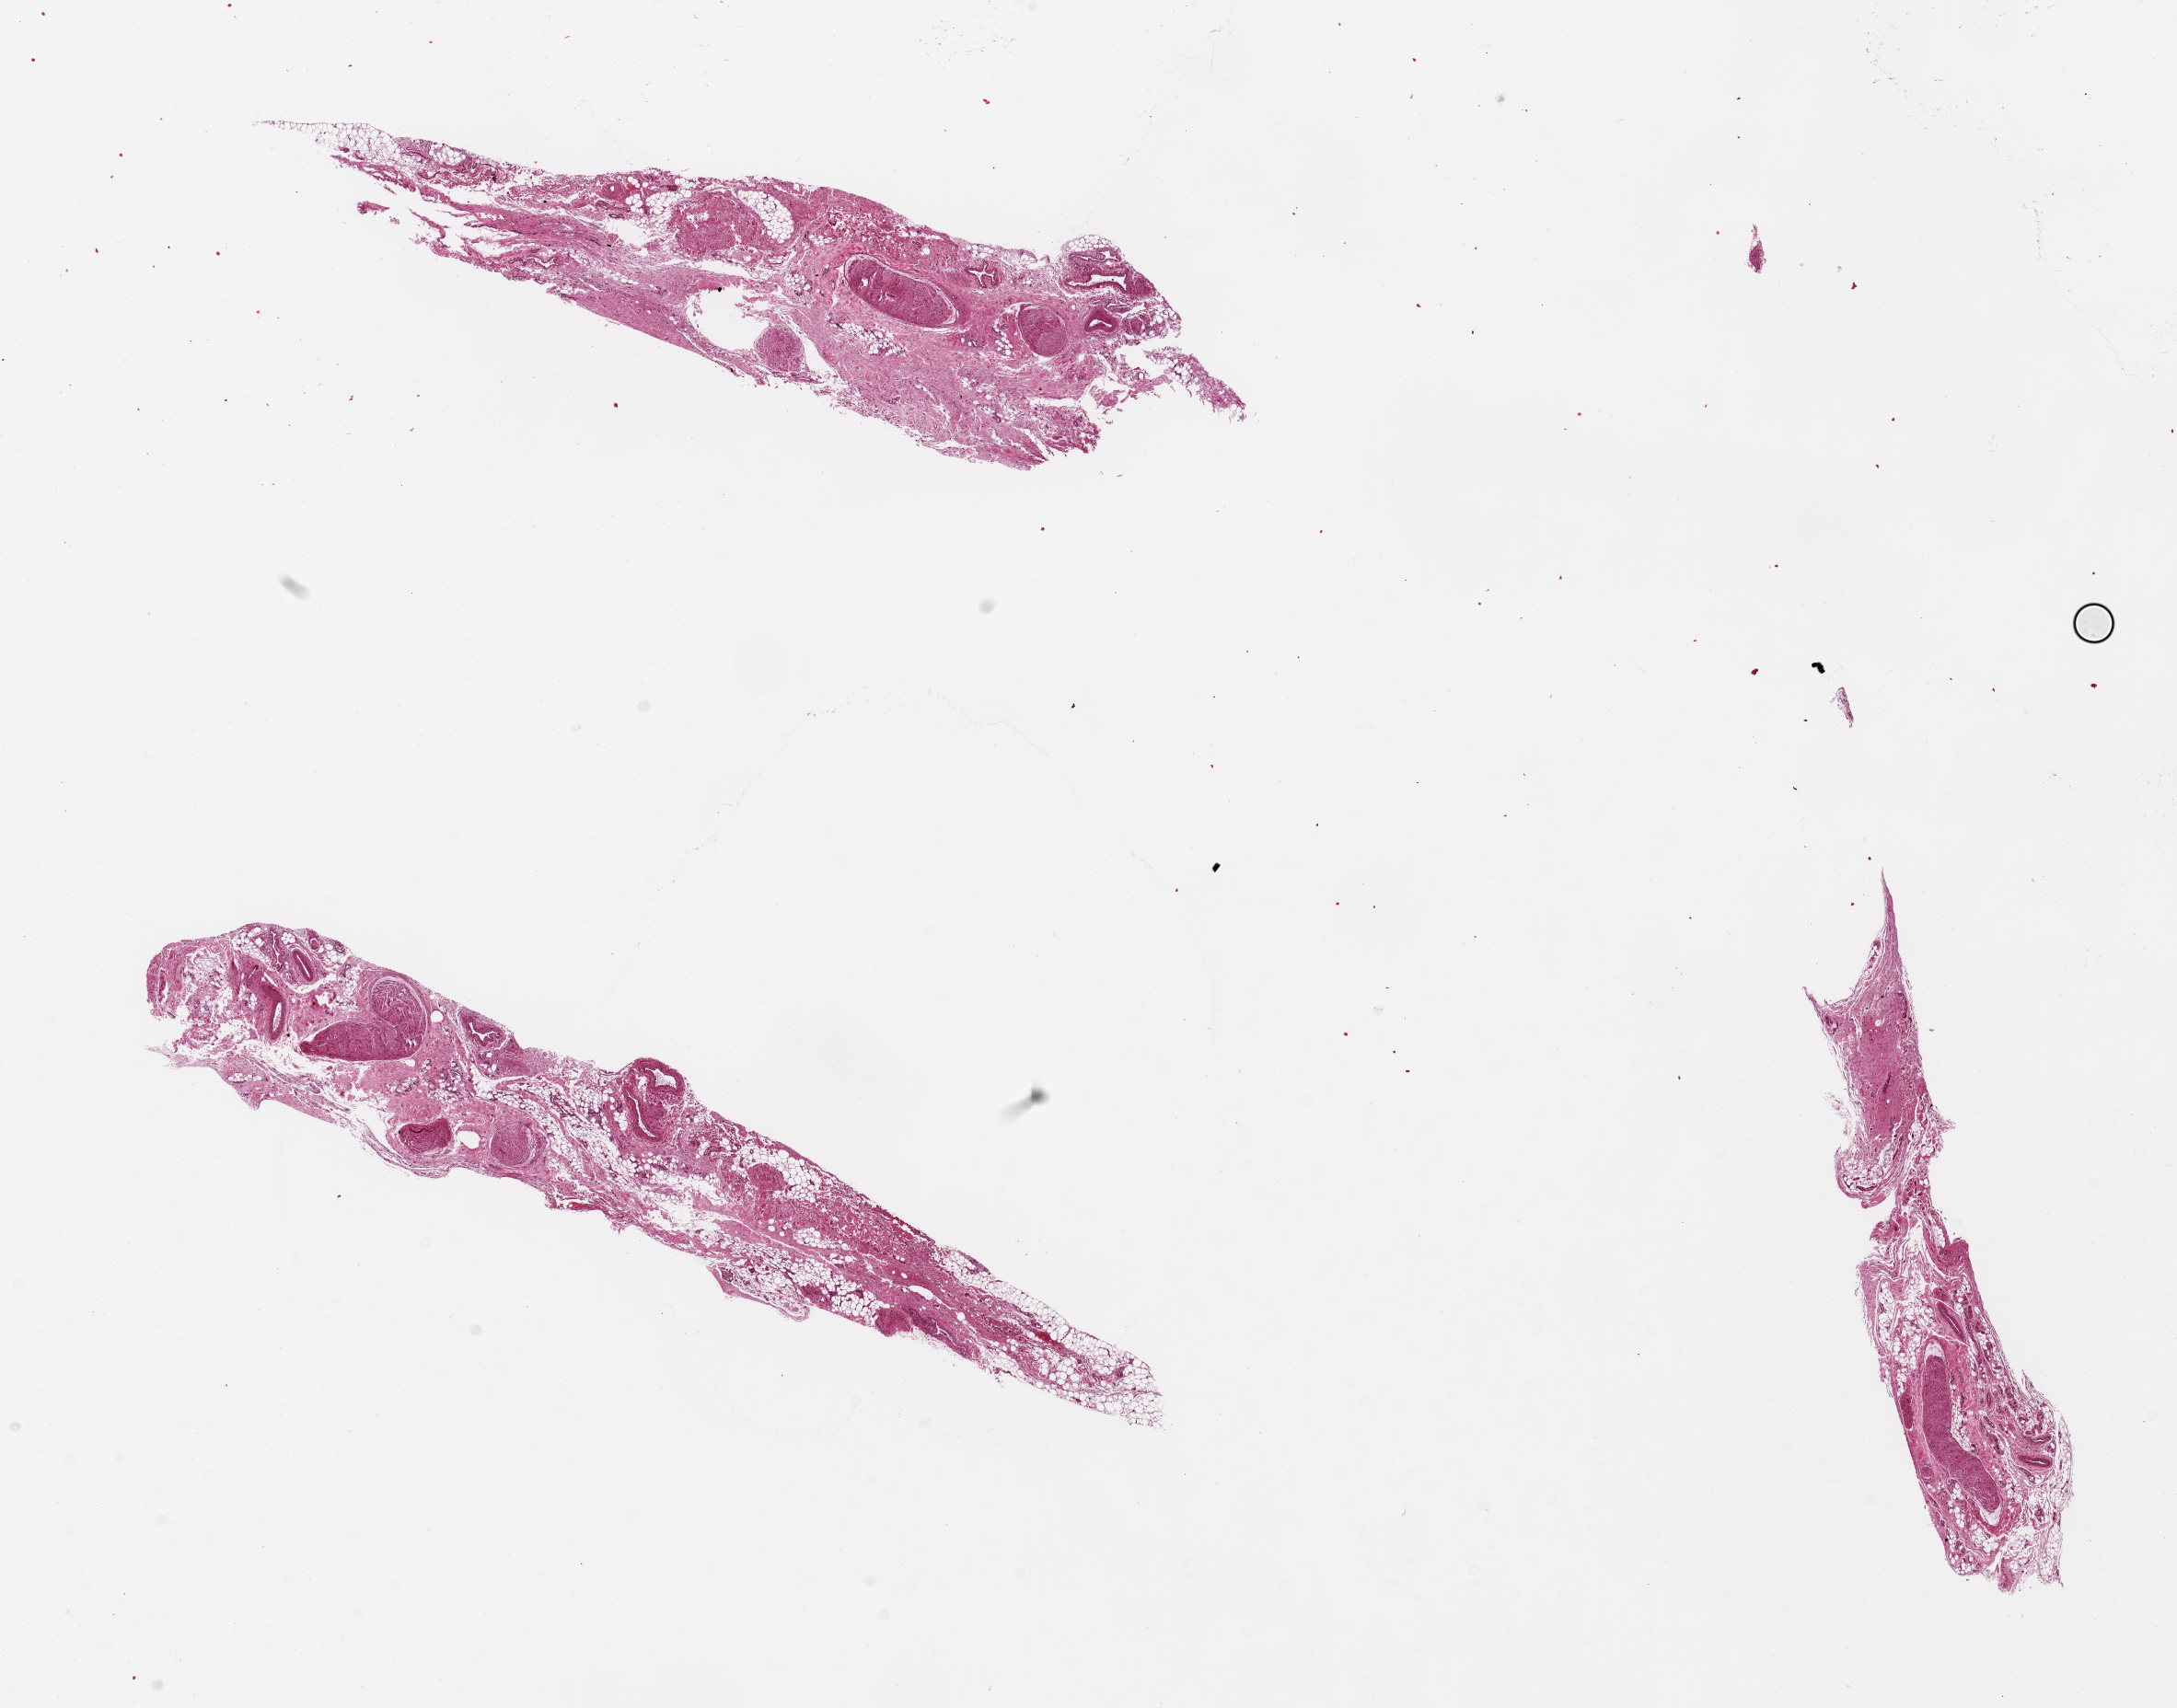
Digitized H&E-stained section, brightfield, low-resolution overview of the scanned area, about 18.7 x 14.7 mm; PAXgene-fixed, paraffin-embedded tissue; section of esophageal mucous membrane (target tissue); donor tissue sample. Donor: male.
- reviewer comment on this tissue sample: 2pieces fibroadipose tissue, uncertain provenance